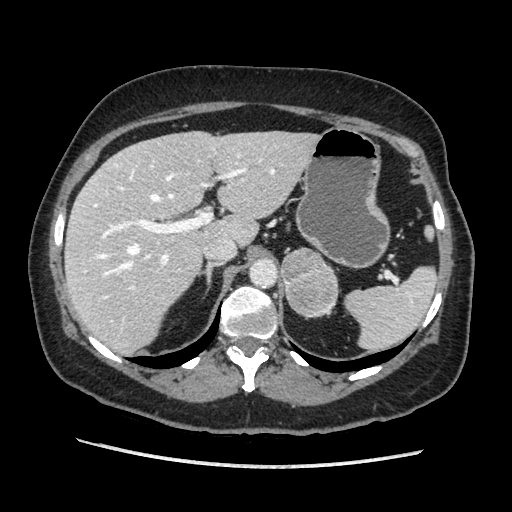
Contrast-enhanced abdominal CT, one axial slice; position 134 of 203 along the scan axis; soft-tissue window (W 400 / L 40 HU); 512 × 512 image matrix, field of view 360 × 360 mm. Female patient. Case-level facts recorded for this patient, not image findings: diagnosis: adrenocortical carcinoma; tumour side: left adrenal; tumour size at pathology: 6.5 cm; Ki-67 index: 22 %; stage (as recorded): 2.
Structures marked on this image (semi-automatically segmented with operator editing):
- mass: bounding box <282,247,339,316> (left, top, right, bottom; pixels)